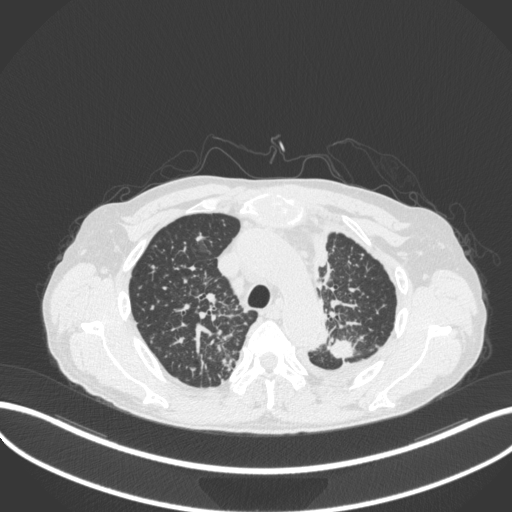
Chest CT, one axial slice; position 266 of 319 along the scan axis; 120 kVp; lung window (W 1500 / L -600 HU); 1 mm slice thickness; 512 × 512 image matrix, field of view 400 × 400 mm. Patient: male, 58 years. Case-level facts recorded for this patient, not image findings: clinical TNM (as recorded): T1c N3 M1.
Outlined on this slice (rectangle marked by the reading radiologist):
- lung tumour (recorded histology: adenocarcinoma): box from (x=326, y=337) to (x=358, y=361) px